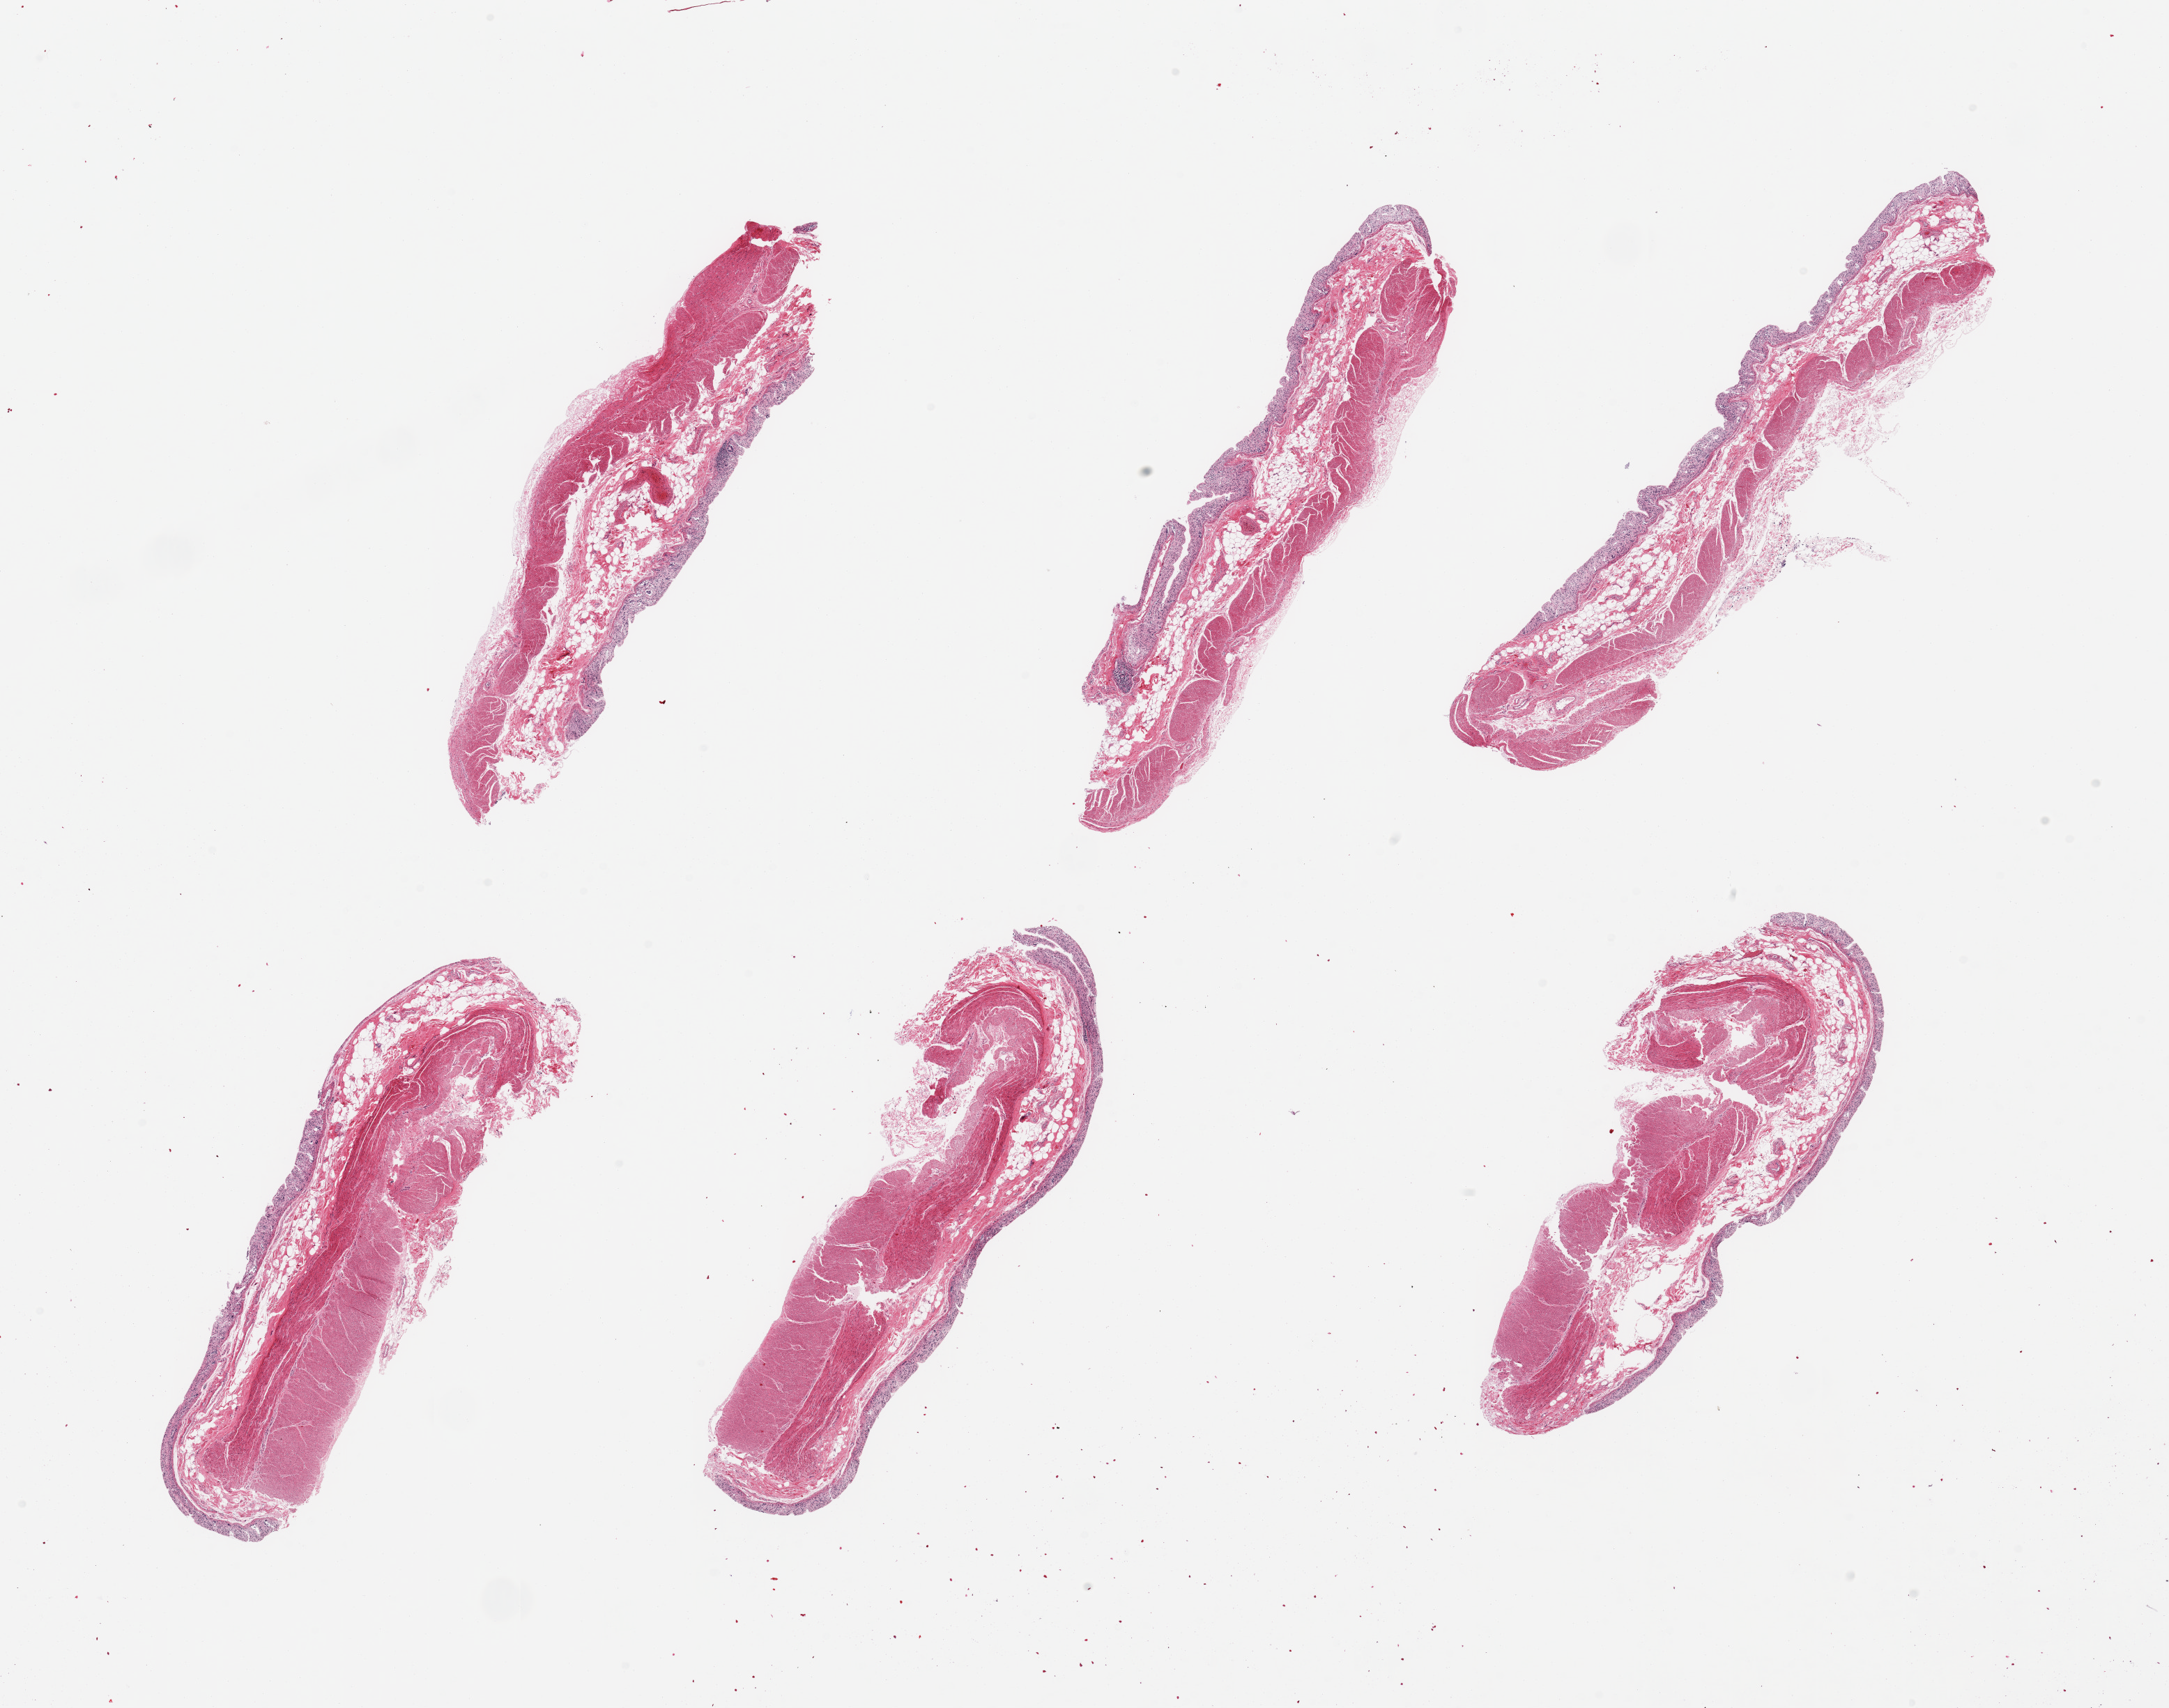
Whole-slide image, H&E stain, shown as a low-resolution overview of the whole scanned area (about 24.6 x 19.4 mm); PAXgene-fixed, paraffin-embedded tissue; target tissue: transverse colon; donor tissue sample.
Review note (as recorded): 6 pieces; mucosa totally autolyzed, muscle intact.